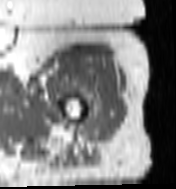
MRI of an extremity soft-tissue mass, one axial slice; slice 91 of 100 in the series (ordered by position); MR volume resampled by the dataset authors to the PET/CT grid (not the native acquisition matrix); 3.27 mm slice thickness; 176 × 189 image matrix, field of view 172 × 185 mm. Female patient. Case-level facts recorded for this patient, not image findings: histological type: undifferentiated – high grade; grade: high; site of the primary tumour: left thigh.
Outlined on this slice (expert contour drawn on MRI and transferred to this co-registered scan by the dataset authors):
- gross tumour volume including surrounding oedema: bounding box (x1, y1, x2, y2) in pixels: (82, 96, 109, 138)